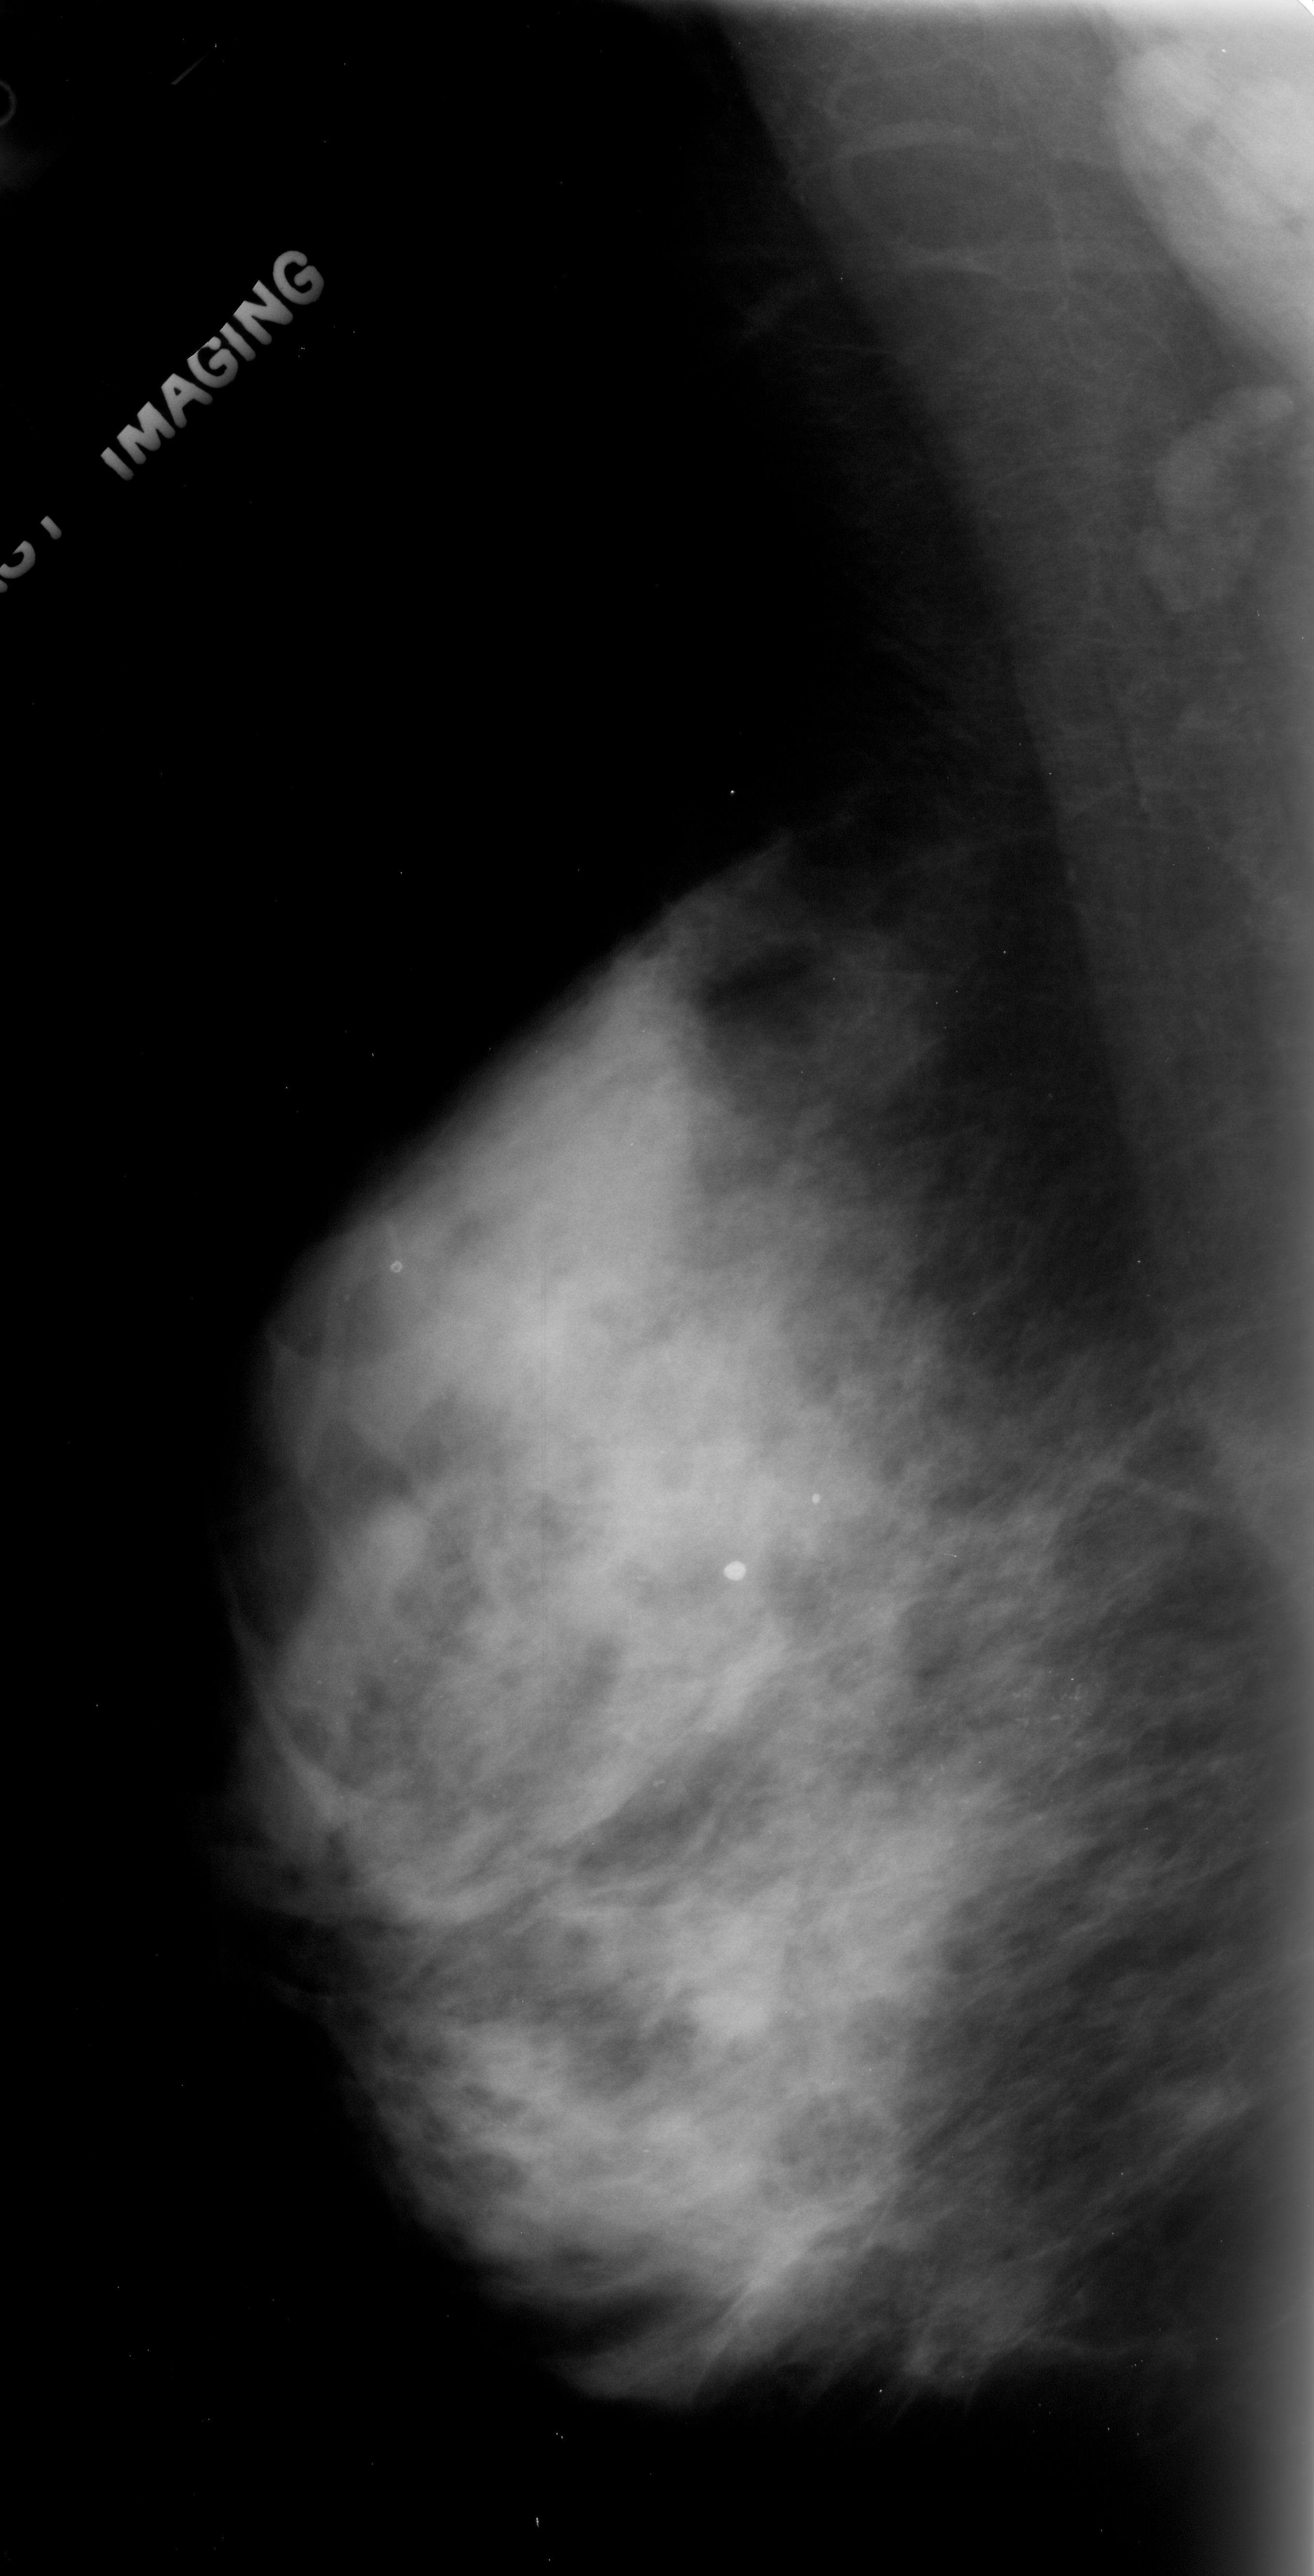
Mammogram (digitized film), left breast, mediolateral oblique (MLO) view.
Finding: calcifications, morphology pleomorphic, distribution linear; BI-RADS assessment category 4; pathology (as recorded): malignant.